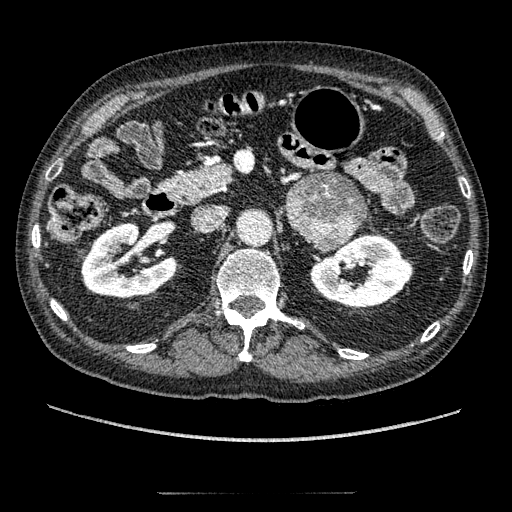
Contrast-enhanced abdominal CT, one axial slice; slice 109 of 274 in the series (ordered by position); reconstruction kernel STANDARD; 120 kVp; intravenous contrast given; soft-tissue window (W 400 / L 40 HU); 1.25 mm slice thickness; 512 × 512 image matrix, field of view 381 × 381 mm. Patient: male, 69 years. Case-level facts recorded for this patient, not image findings: diagnosis: adrenocortical carcinoma; tumour side: left adrenal; tumour size at pathology: 6.1 cm; Ki-67 index: 10 %; stage (as recorded): 3.
Annotated regions visible in this slice (semi-automatic segmentation, software-assisted and operator-edited):
- mass: bounding box <288,173,366,251> (left, top, right, bottom; pixels)